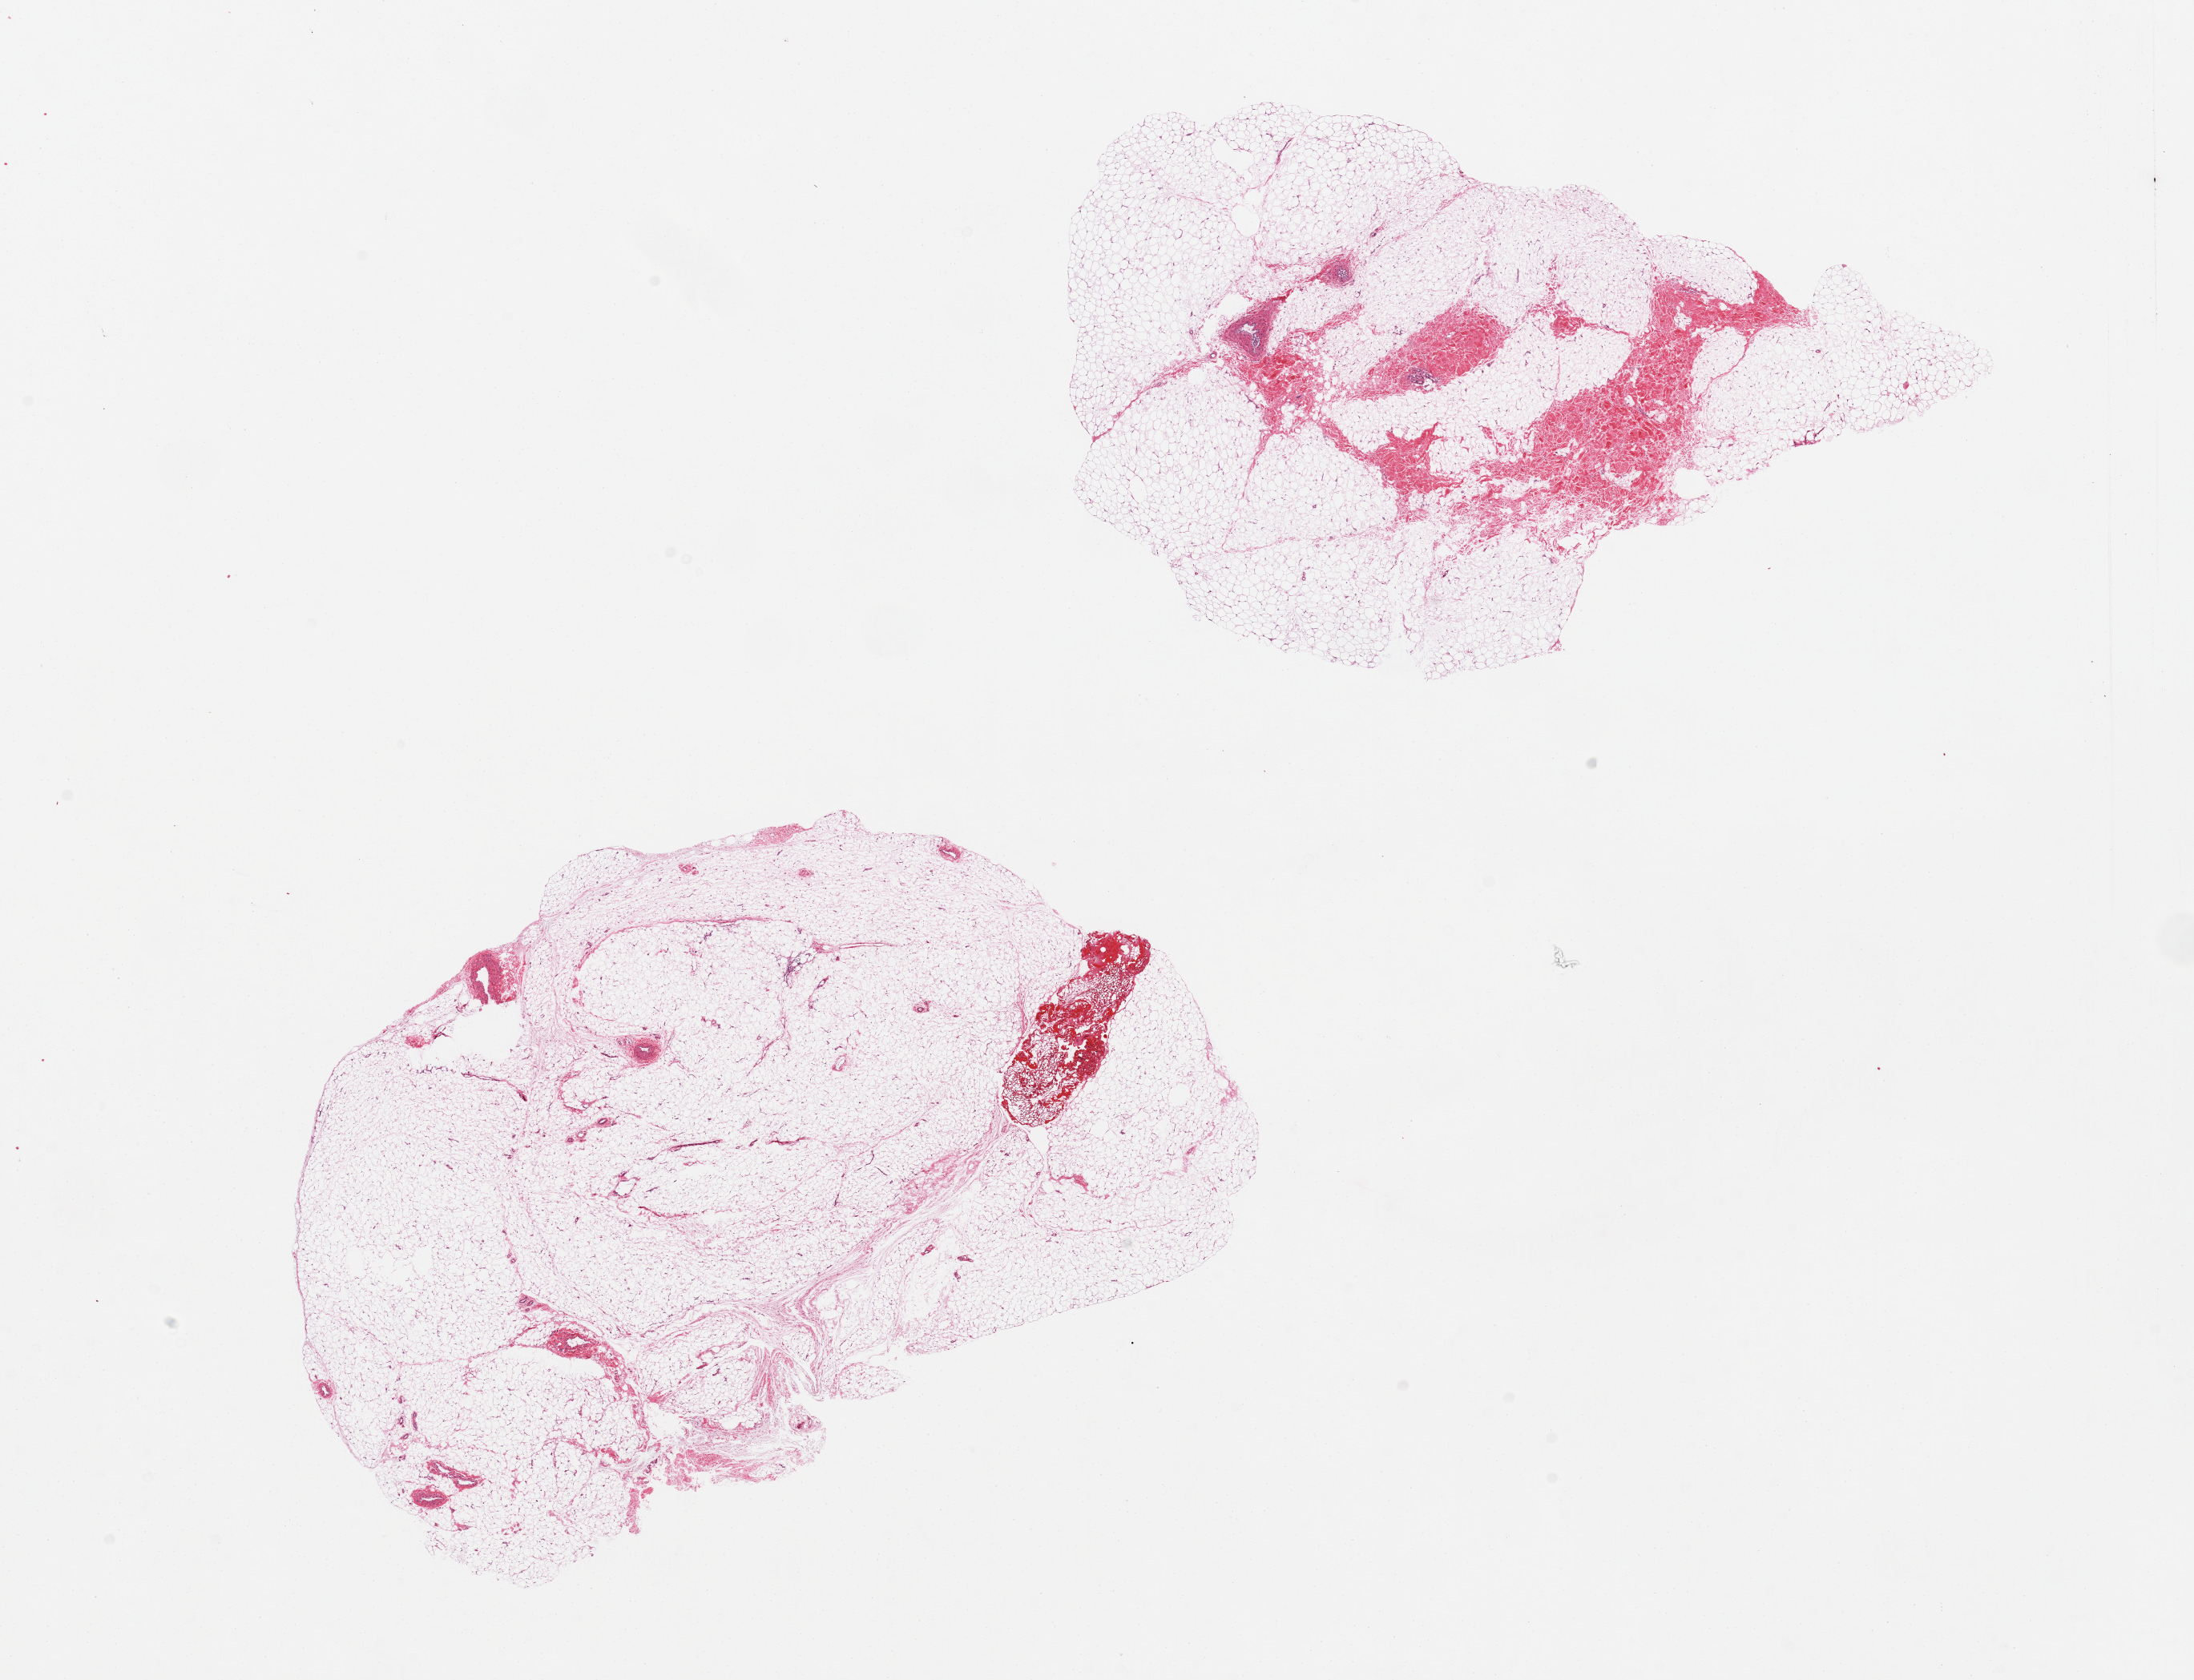
Digitized H&E-stained section, shown as a low-resolution overview of the whole scanned area (about 21.7 x 16.6 mm, from a 20x scan); PAXgene-fixed paraffin-embedded (PFPE) section; target tissue: adipose tissue; tissue donor sample.
Pathologist's review note for this sample: 2 pieces, one is ~10% fibrous with few sweat glands.